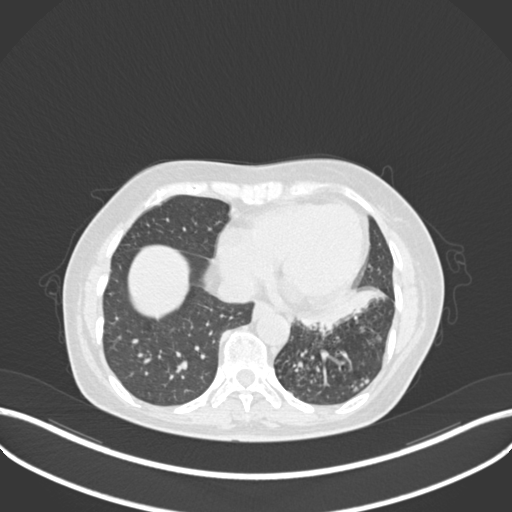
Chest CT, one axial slice; position 82 of 270 along the scan axis; reconstruction kernel B30f; 120 kVp; lung window (W 1500 / L -600 HU); 1 mm slice thickness; 512 × 512 image matrix, field of view 400 × 400 mm. Patient: female, 63 years. Case-level facts recorded for this patient, not image findings: clinical TNM (as recorded): T1b N0 M0; histopathological grade: G2-3.
Structures marked on this image (bounding box drawn by a radiologist):
- lung tumour (recorded histology: adenocarcinoma): box from (x=294, y=290) to (x=386, y=331) px